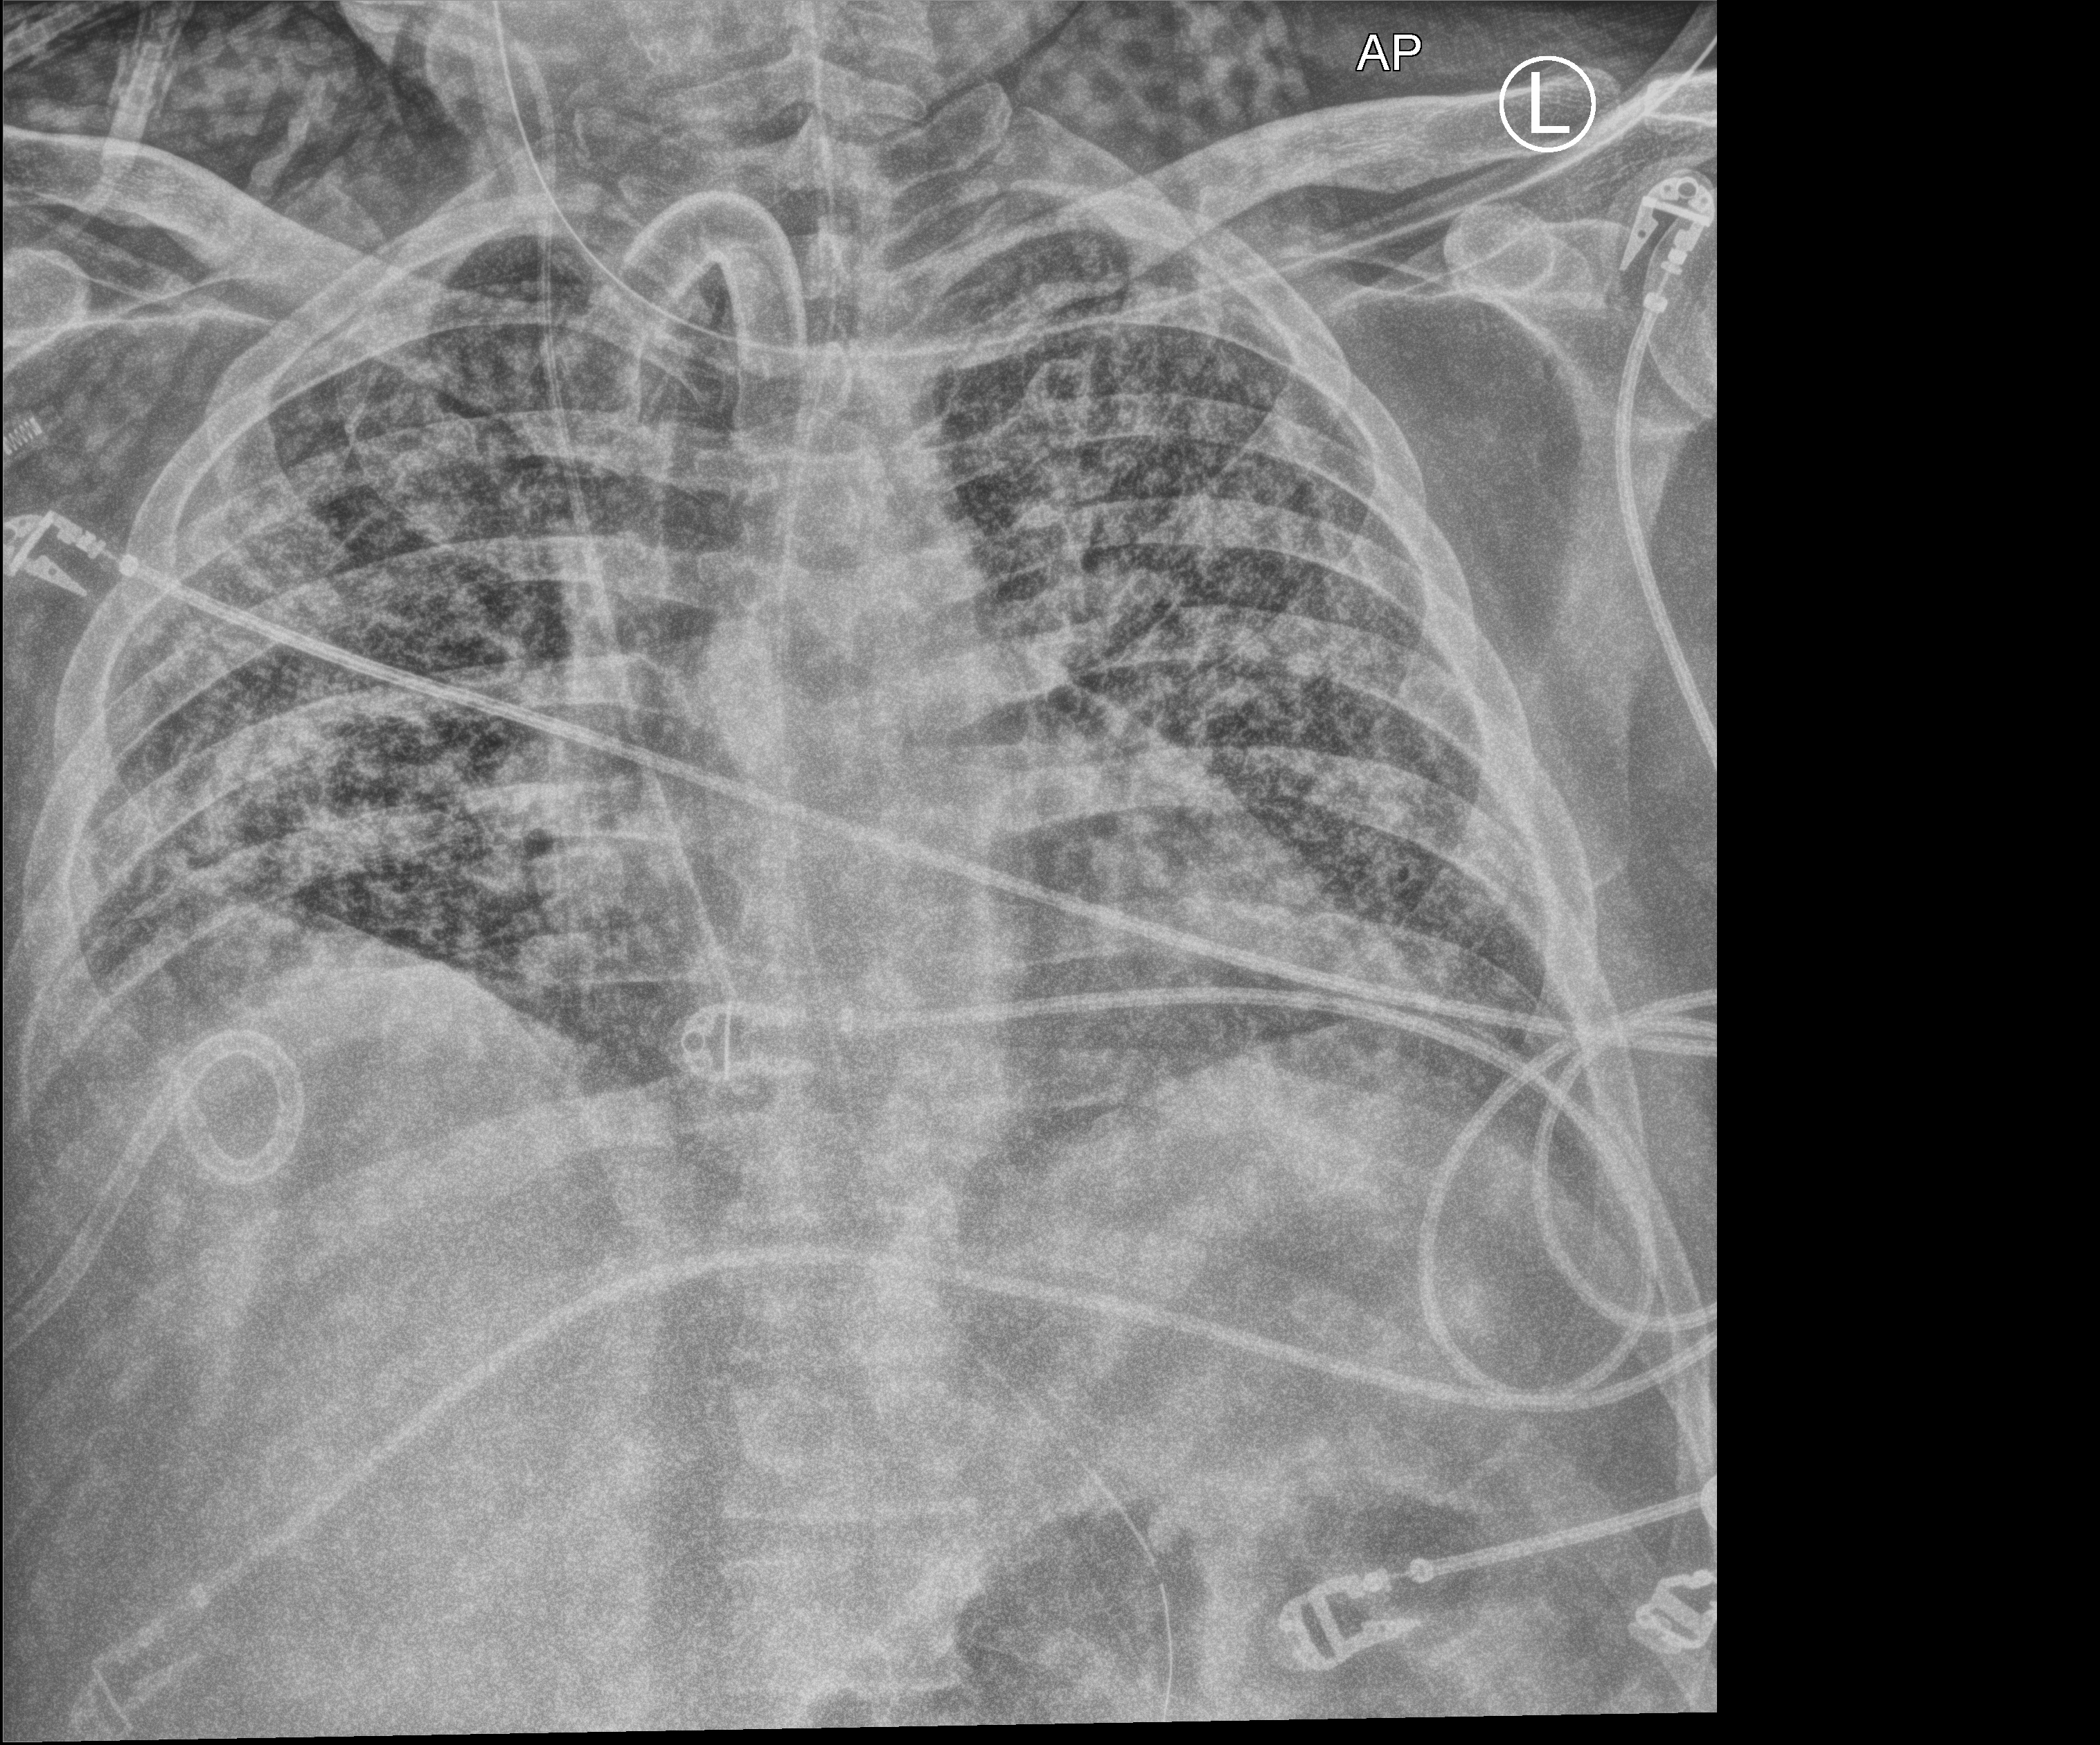
Bedside chest radiograph (computed radiography), anteroposterior (AP) projection. Patient hospitalised with COVID-19; male, aged 18–59 years.
From the hospital-stay record, not from the radiograph (when in the stay this image was taken is not recorded): hypertension (admission record): yes; mechanically ventilated during this hospital stay: yes.